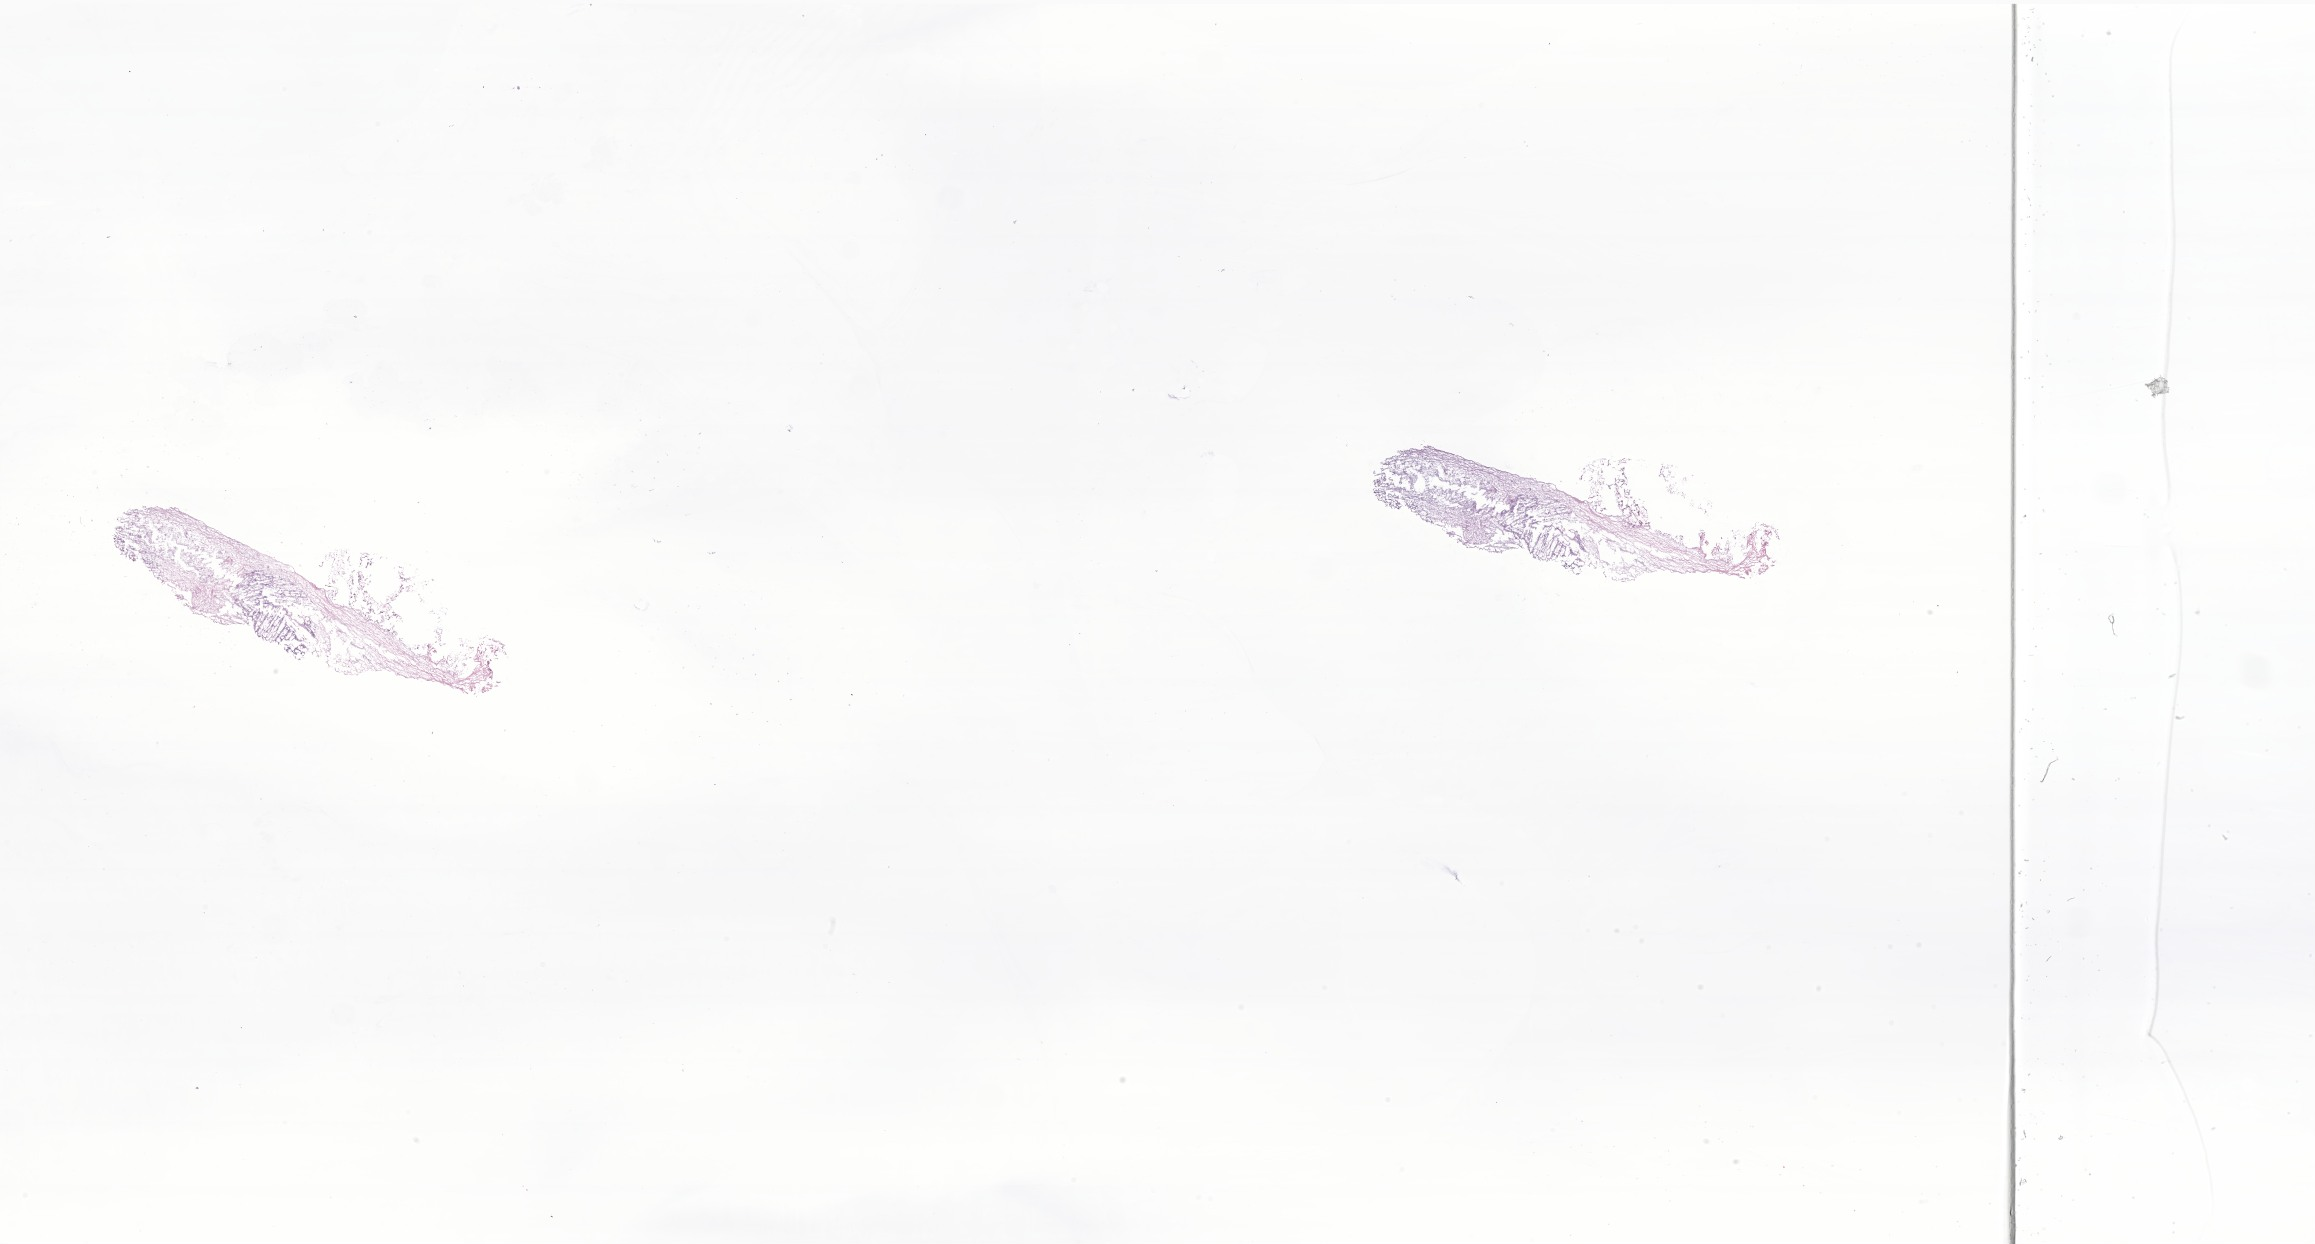
H&E whole-slide image of tumor tissue from the adrenal gland, whole scanned area (about 39.0 x 21.0 mm) shown as a low-resolution overview. Frozen section (OCT-embedded). Patient female; age 758 days (about 2.1 years).
Diagnosis: Neuroblastoma, NOS.